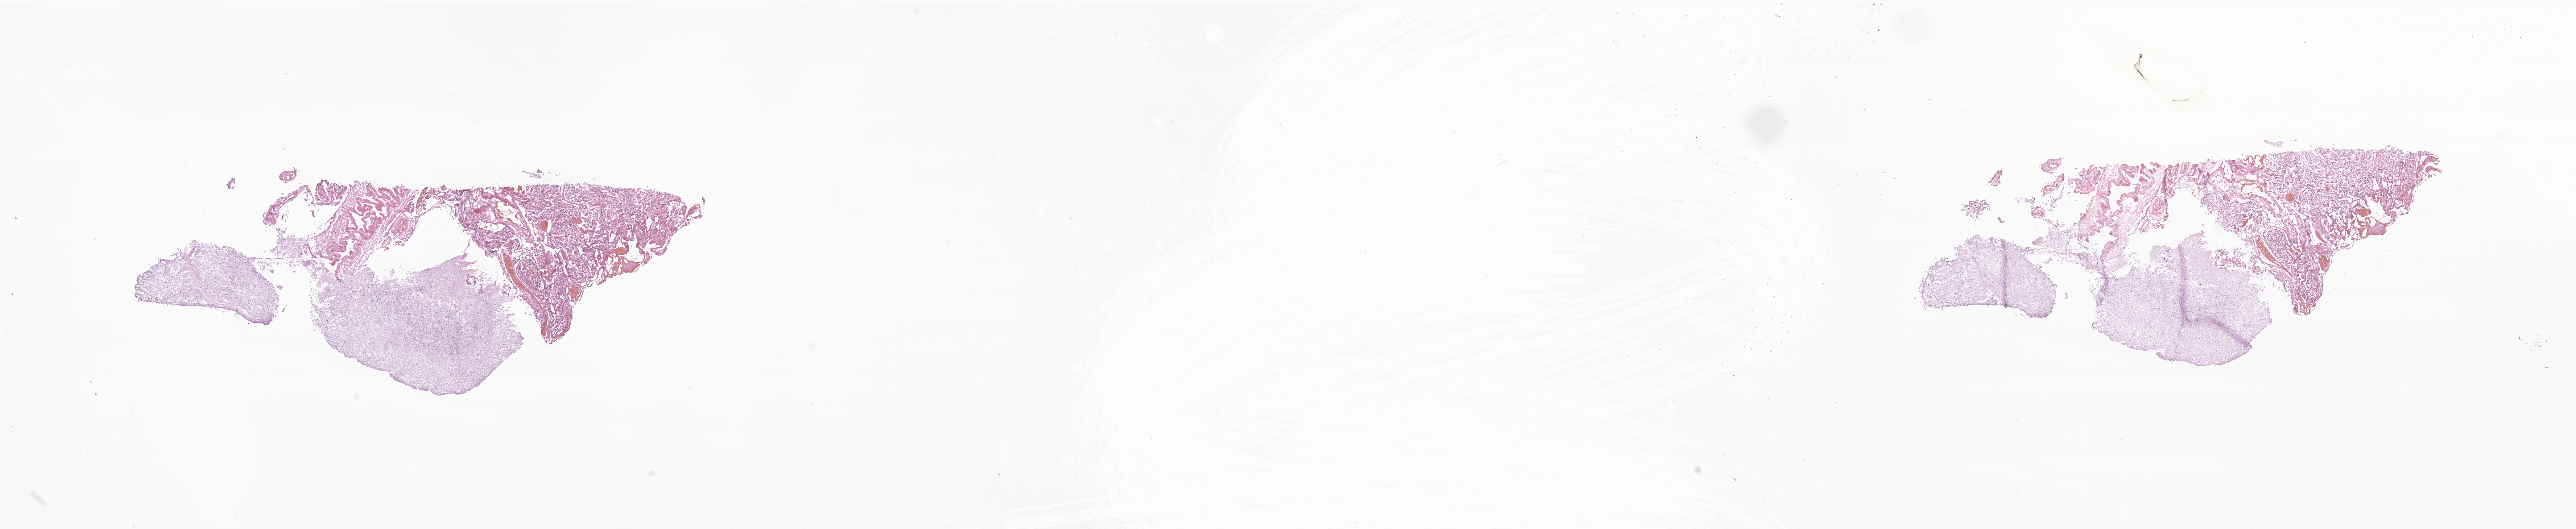
Digitized haematoxylin and eosin-stained section of tumor tissue from the brain, low-resolution overview of the scanned area, about 35.2 x 7.2 mm; cryosection (OCT / tissue freezing medium). Patient male; age 91 months (7 years 7 months).
Diagnosis: Ganglioglioma, NOS.